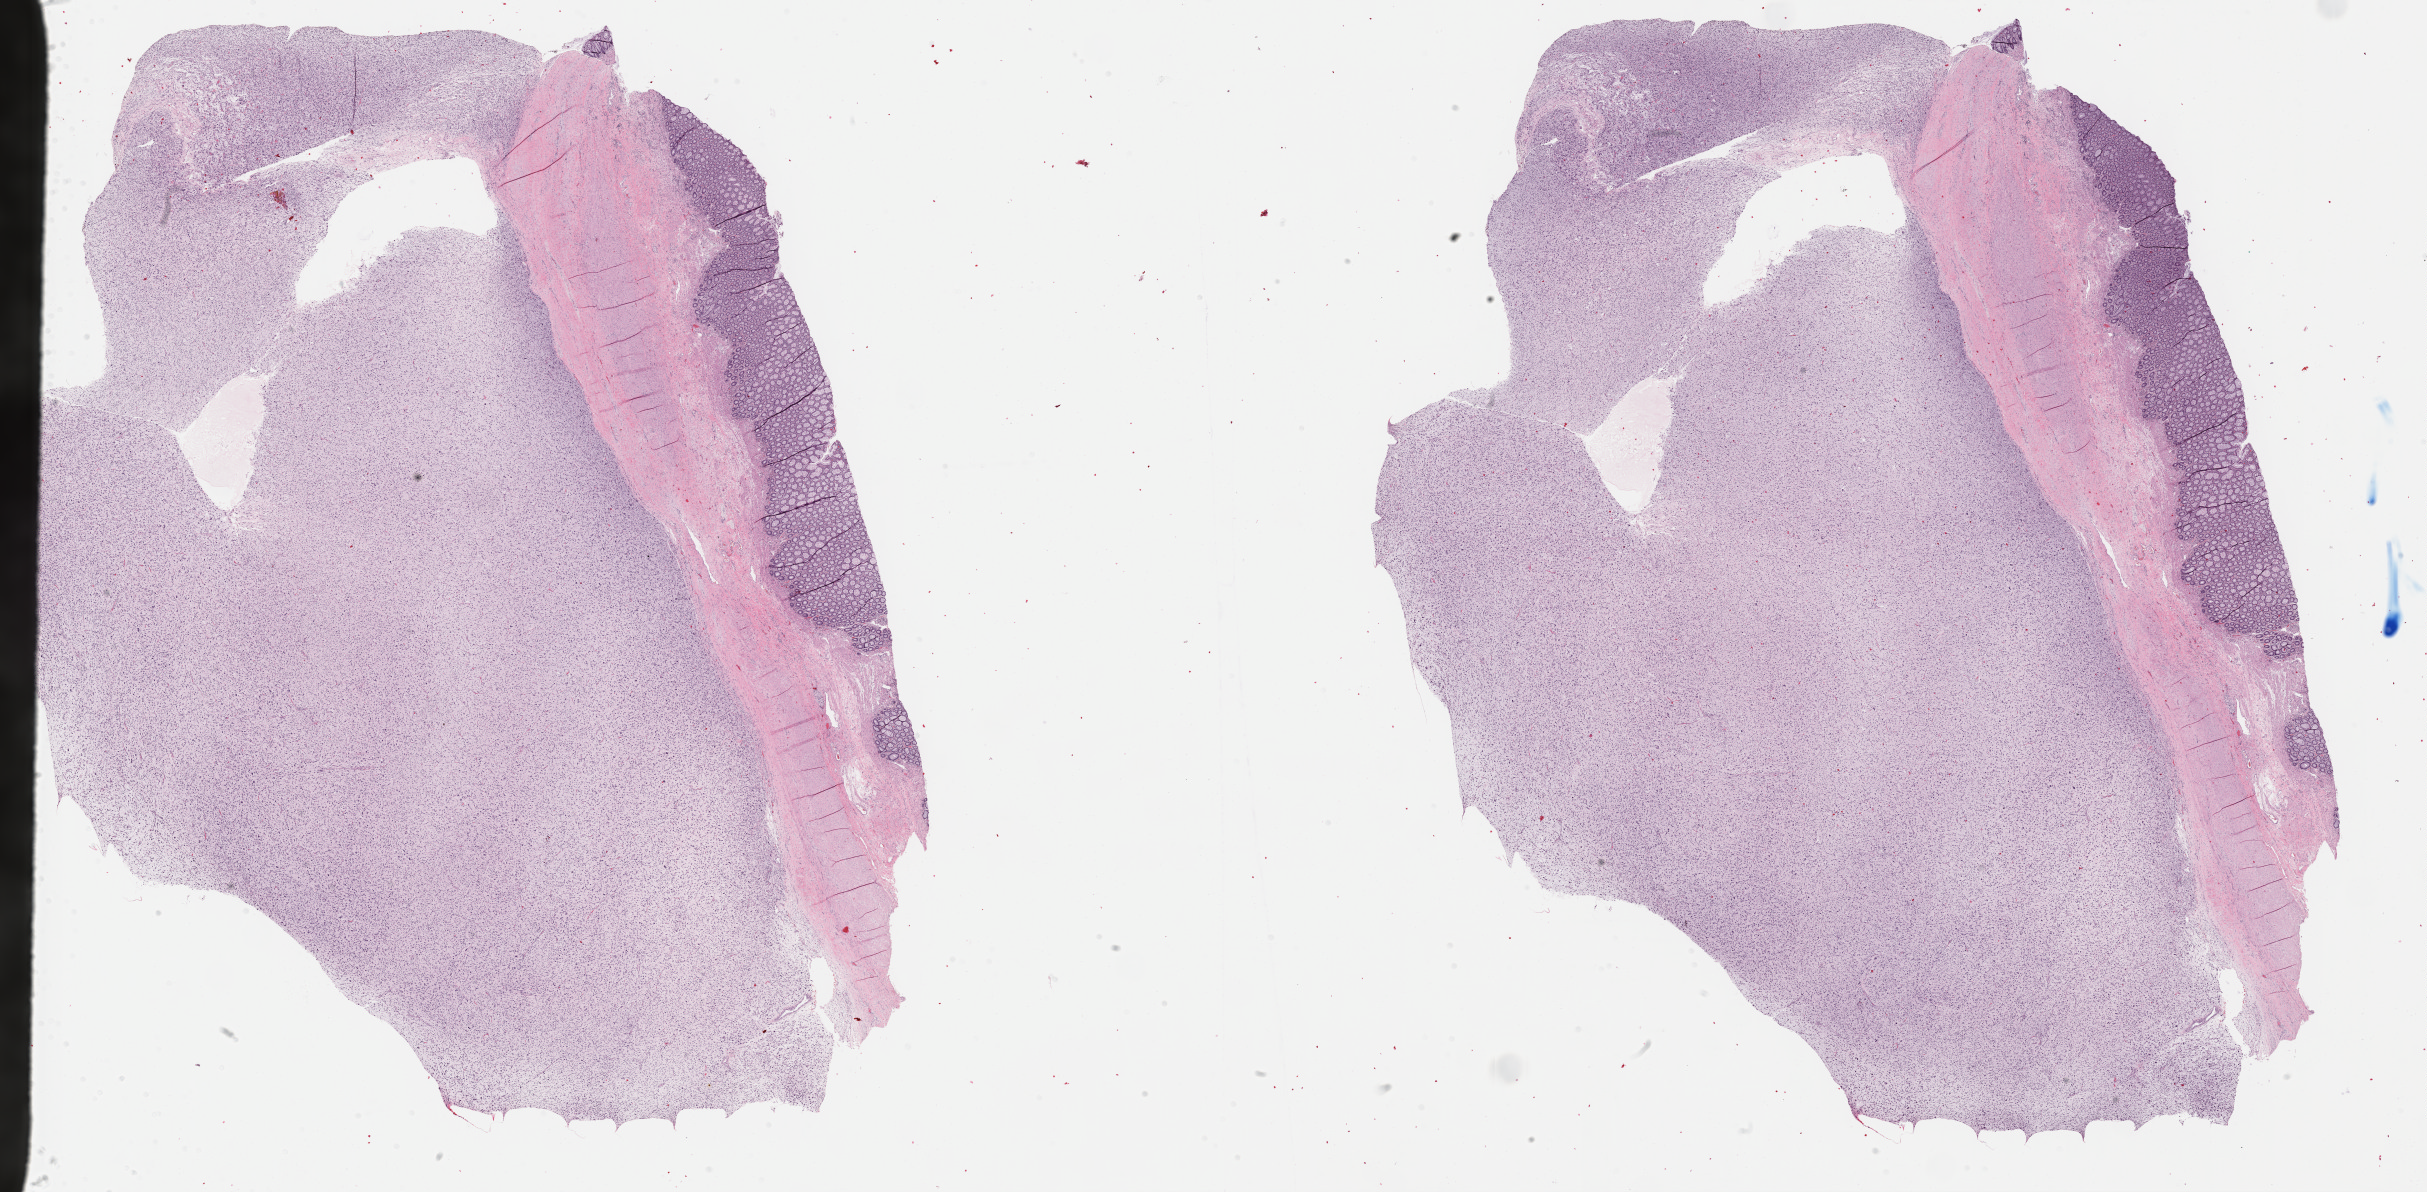
Whole-slide histology image, Hematoxylin and eosin (H&E) stained — shown as a low-resolution overview of the whole scanned area (about 39.3 x 19.3 mm, from a 40x scan); FFPE section; primary tumour sample from the colon. Male patient; age at initial diagnosis 65 years.
Diagnosis: Dedifferentiated liposarcoma.